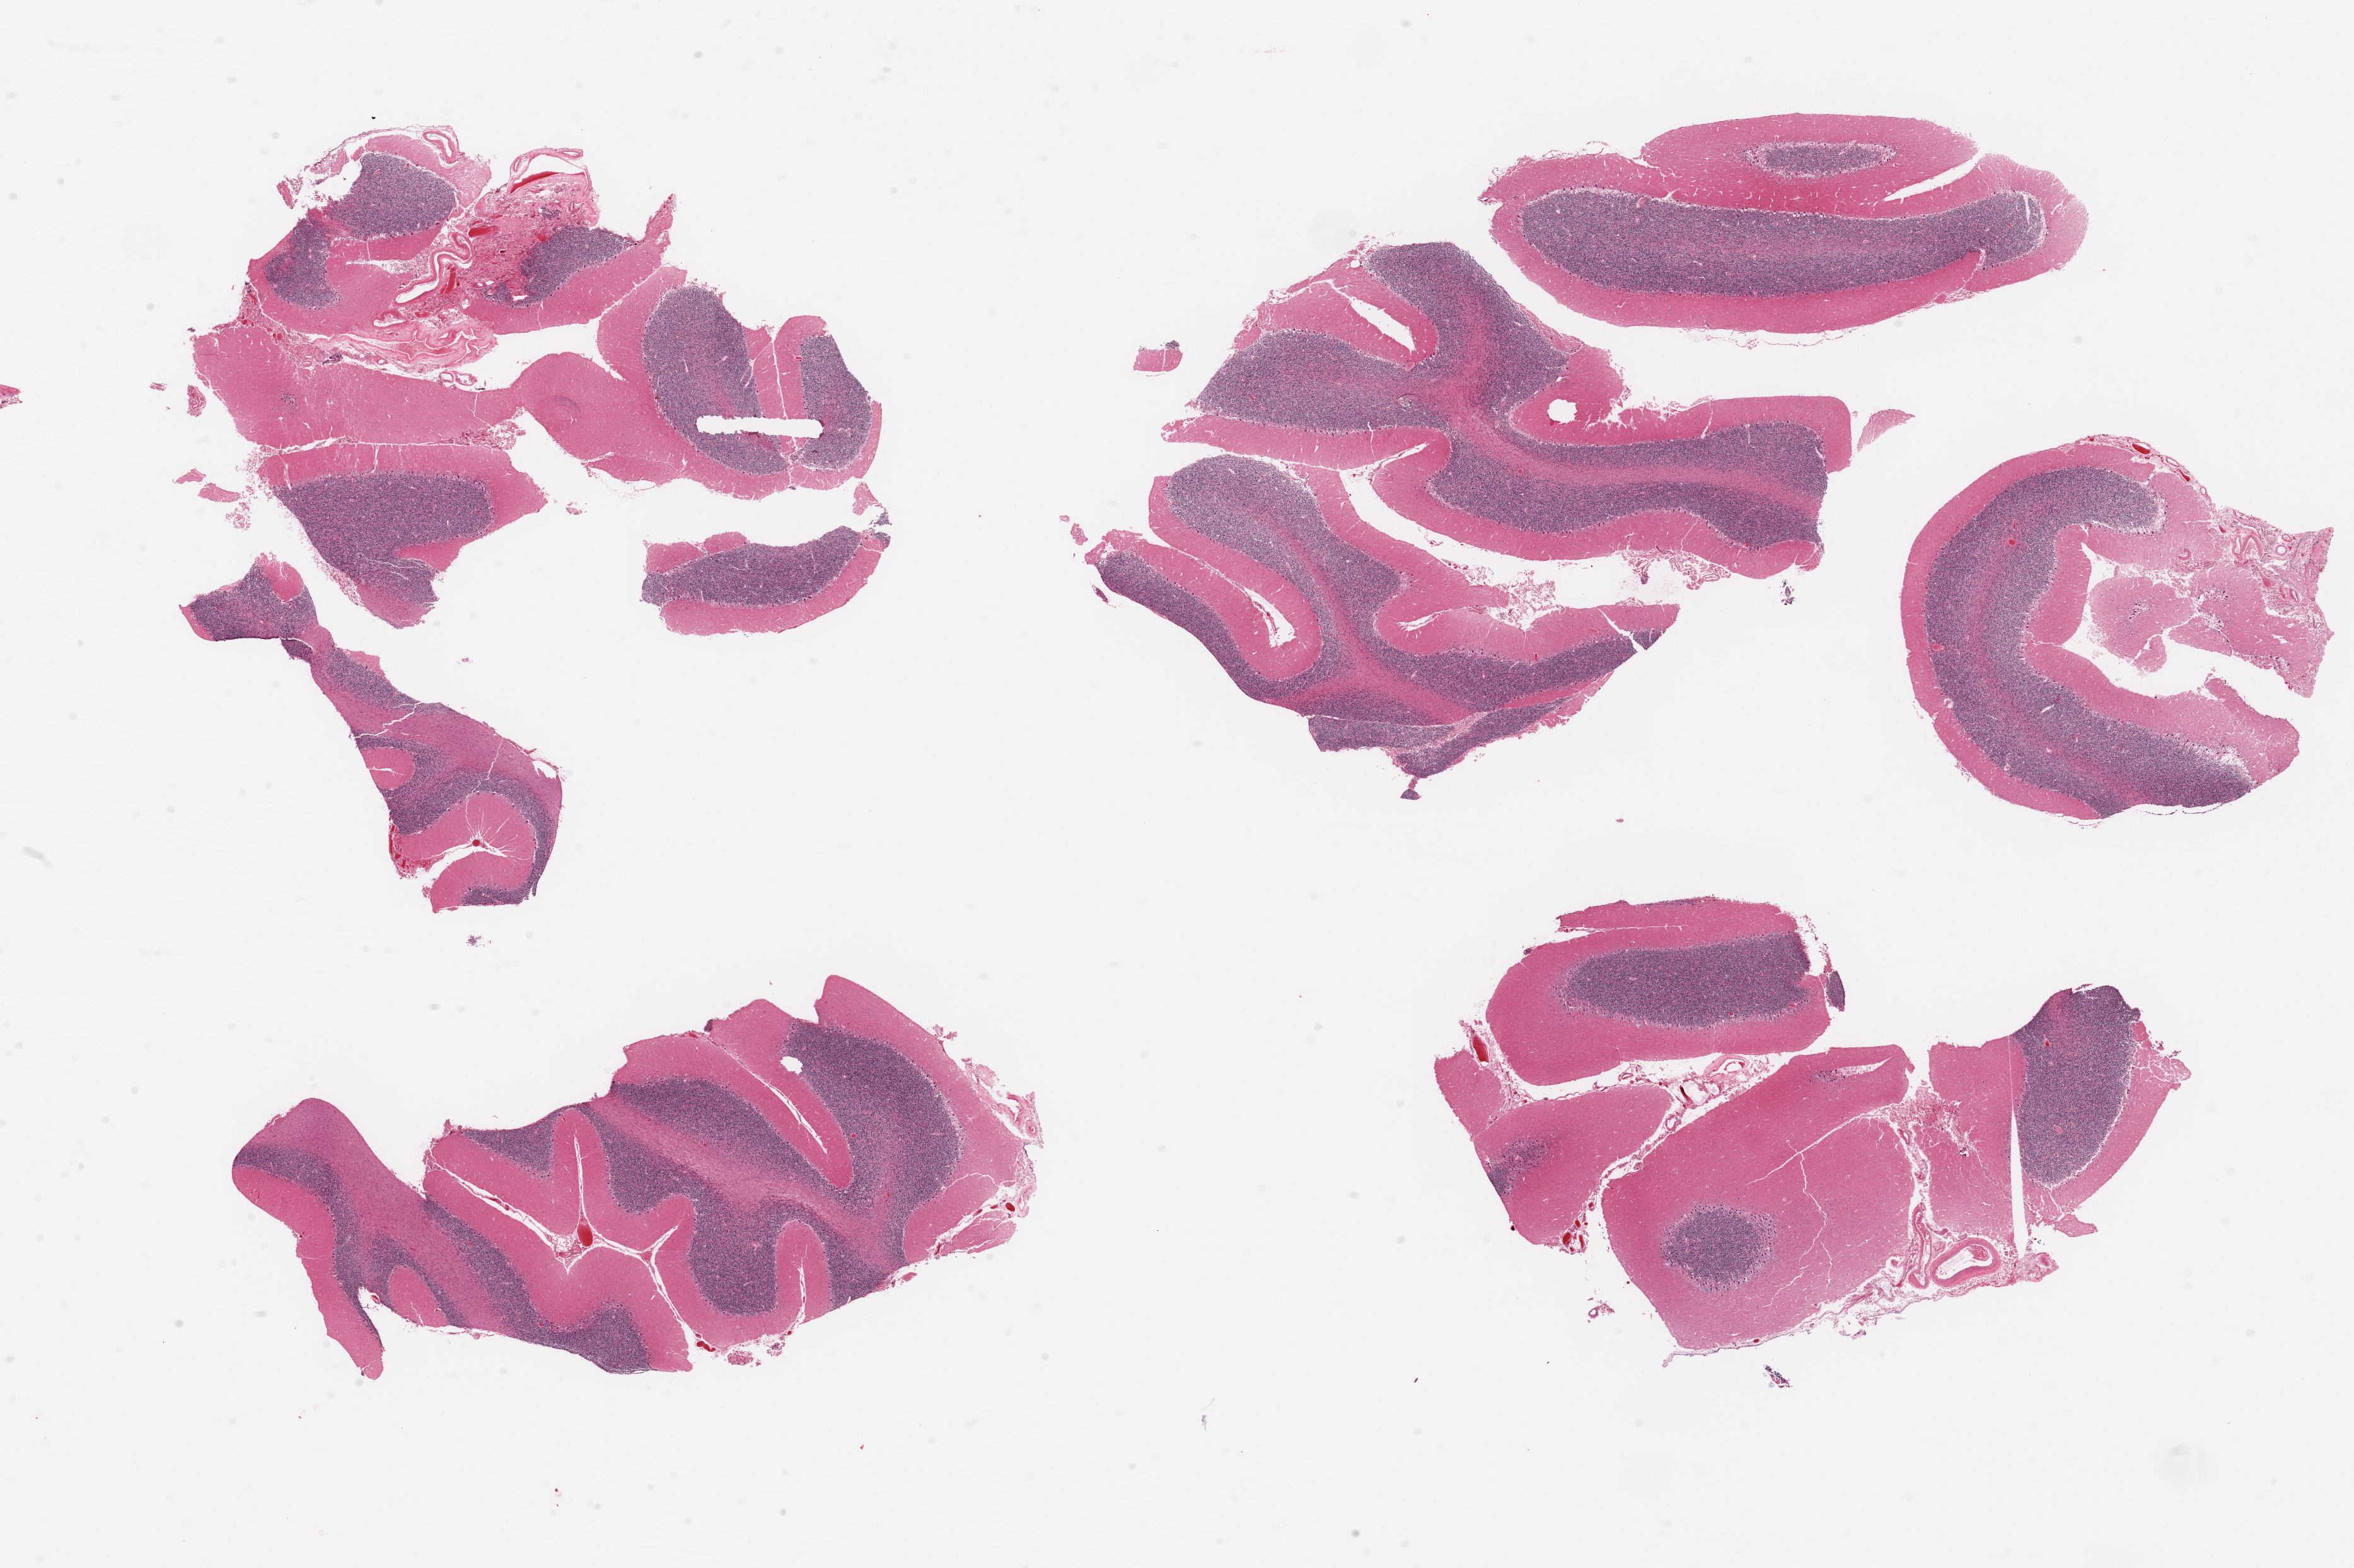
Haematoxylin and eosin whole-slide image, brightfield — shown as a low-resolution overview of the whole scanned area (about 29.5 x 19.7 mm, acquisition: 20x scan). PAXgene-fixed paraffin-embedded (PFPE) section. Sampled site (target tissue): cerebellum. Tissue donor sample. Donor sex: male.
- review note (as recorded): 4 pieces (fragmented) no abnormalities